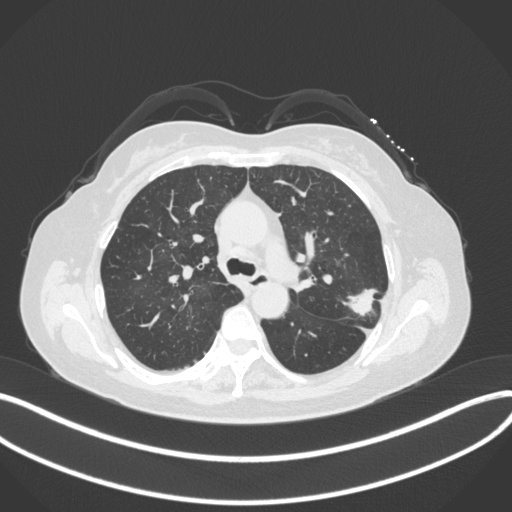
Chest CT, one axial slice; slice 226 of 330 in the series (ordered by position); reconstruction kernel B31f; 120 kVp; lung window (W 1500 / L -600 HU); 1 mm slice thickness; 512 × 512 image matrix, field of view 400 × 400 mm. Female patient, age 60 years. From the clinical record (not read from this slice): clinical TNM (as recorded): T1c N0 M0.
Structures marked on this image (rectangle marked by the reading radiologist):
- lung tumour (recorded histology: adenocarcinoma): bounding box <343,281,380,318> (left, top, right, bottom; pixels)